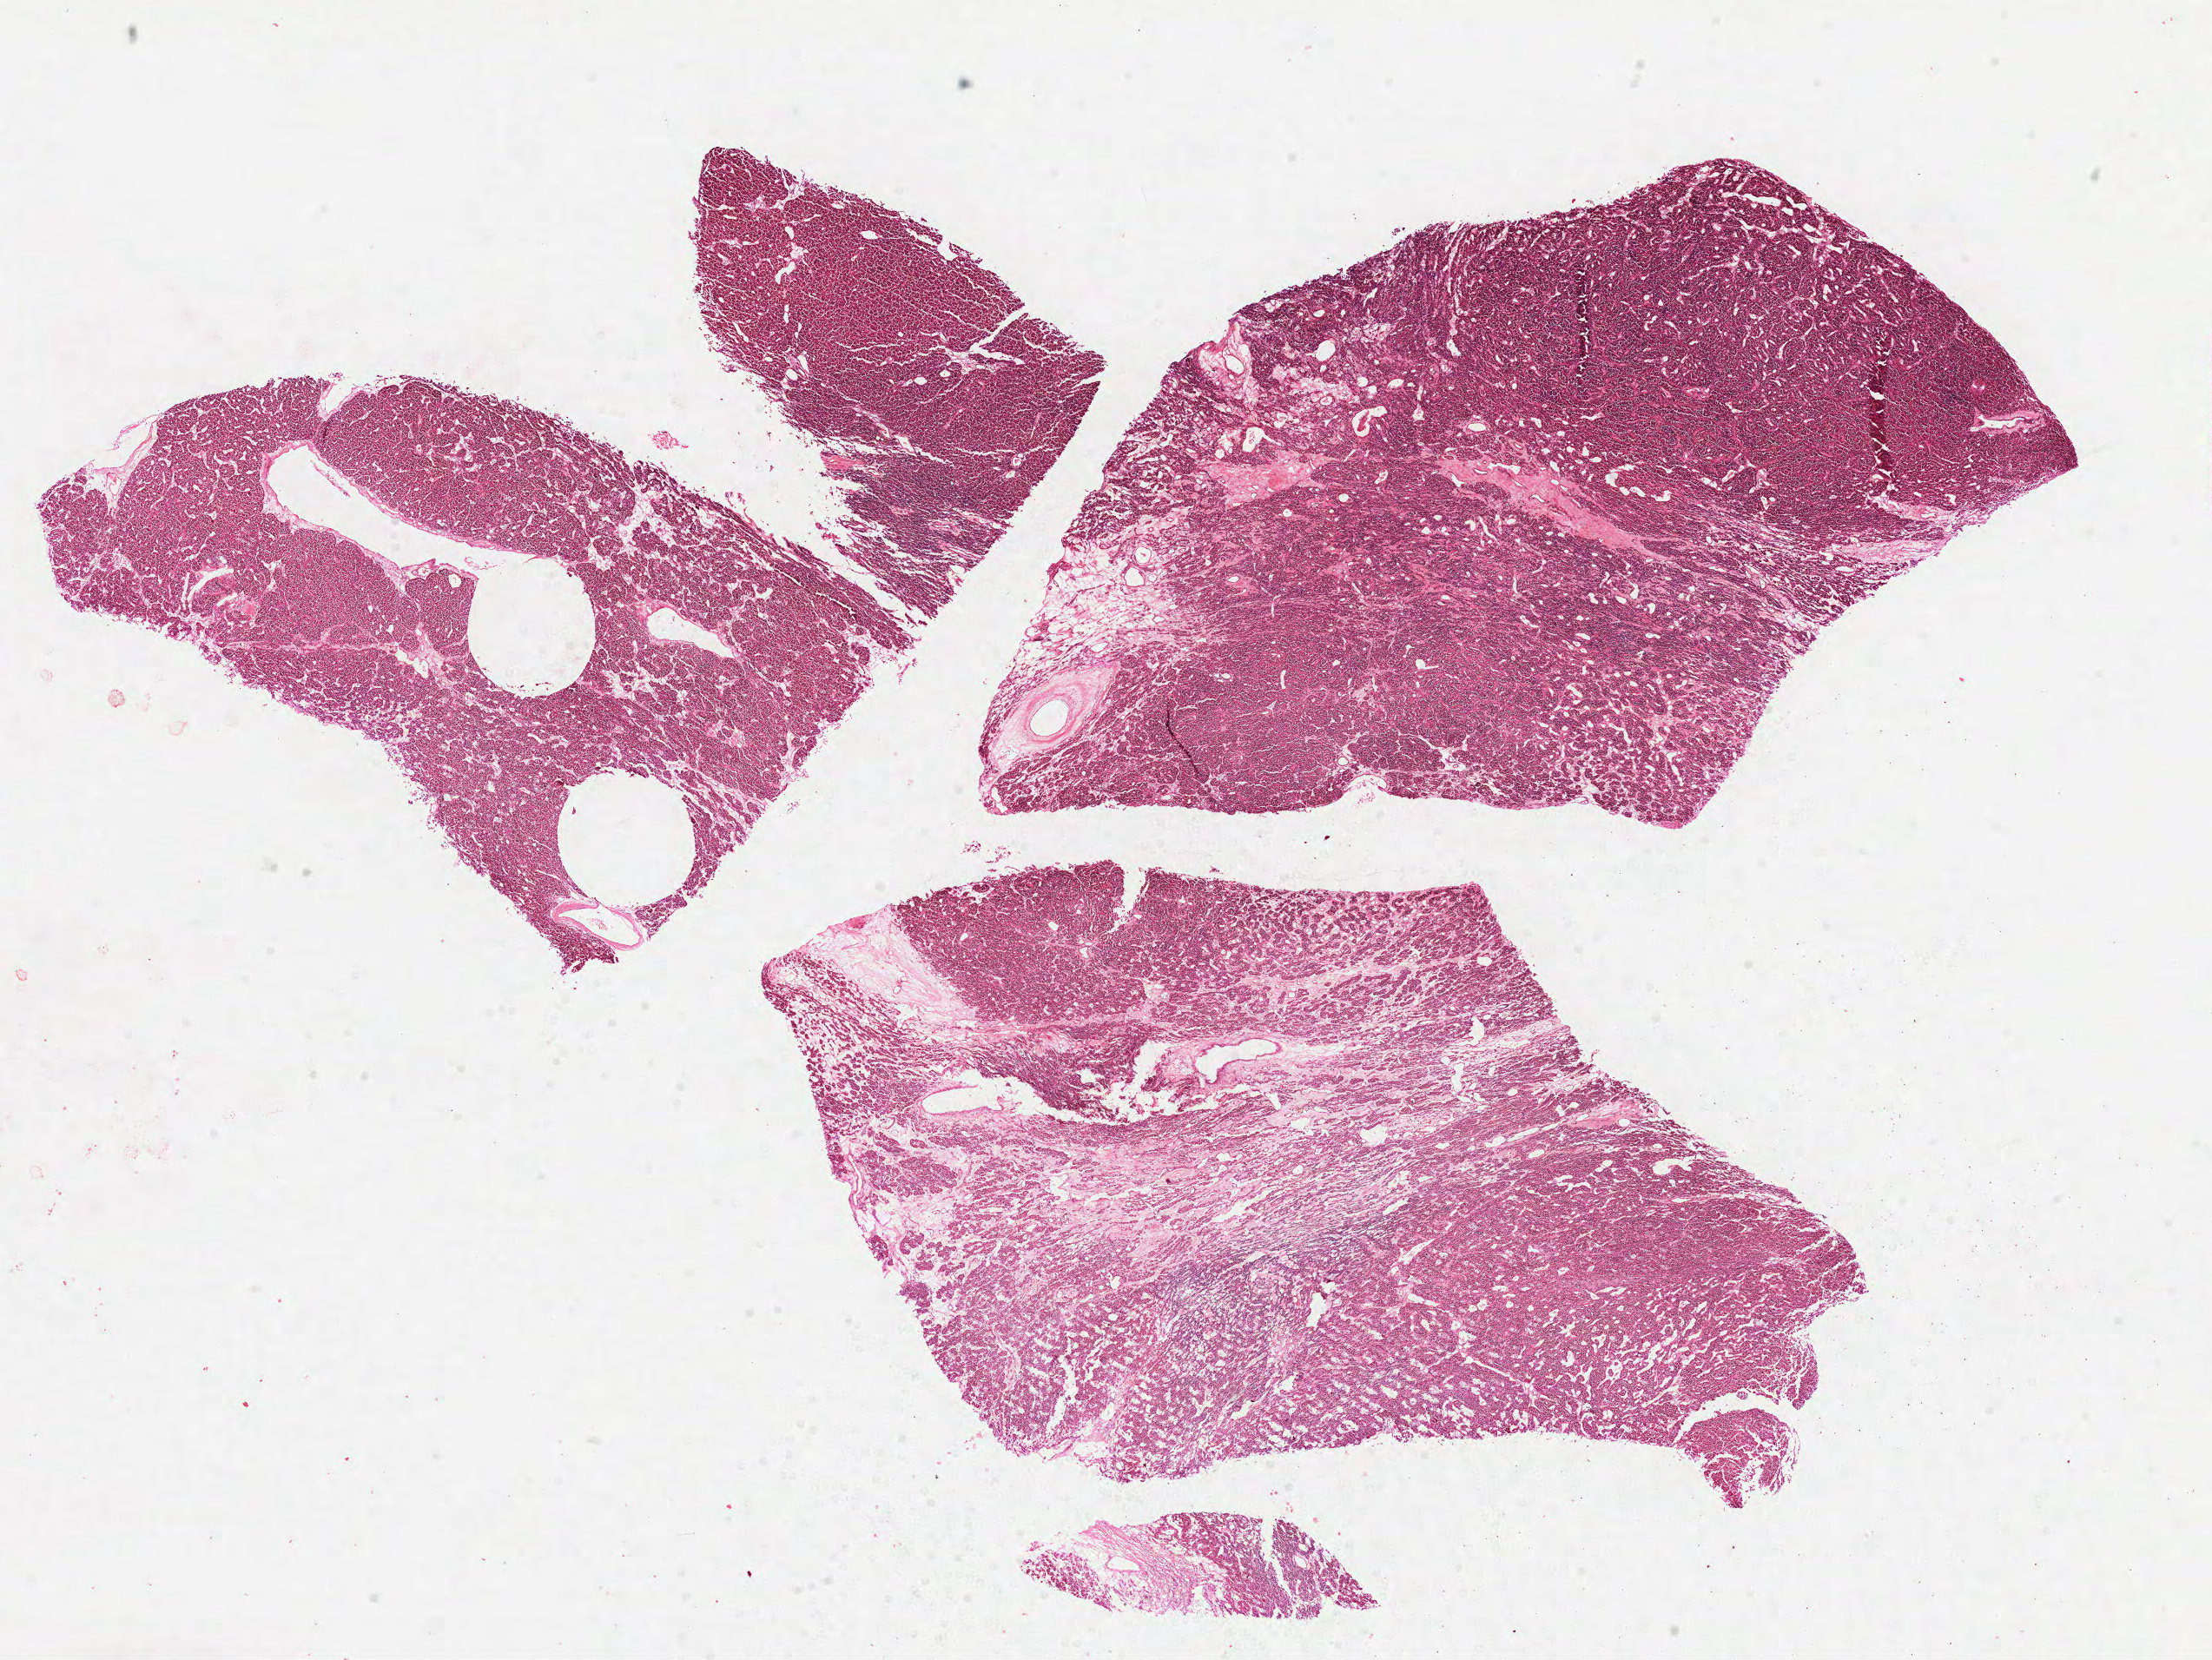
Whole-slide histology image, H&E, low-resolution overview of the scanned area, about 20.5 x 15.4 mm (from a 40x scan). FFPE section. Primary tumour sample from the kidney. Male patient; age at initial diagnosis 65 years.
Diagnosis: Clear cell adenocarcinoma, NOS.